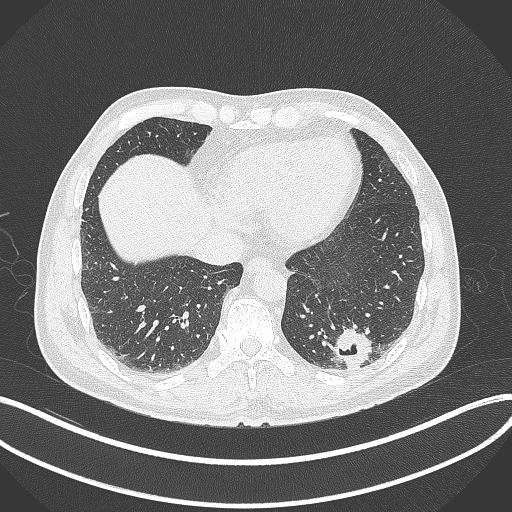
Chest CT, one axial slice; slice 74 of 300 in the series (ordered by position); 120 kVp; lung window (W 1500 / L -600 HU); 1 mm slice thickness; 512 × 512 image matrix, field of view 400 × 400 mm. Patient: male, 54 years. From the clinical record (not read from this slice): clinical TNM (as recorded): T1c N0 M1; histopathological grade: G3.
Structures marked on this image (bounding box drawn by a radiologist):
- lung tumour (recorded histology: adenocarcinoma): bounding box <333,322,373,372> (left, top, right, bottom; pixels)